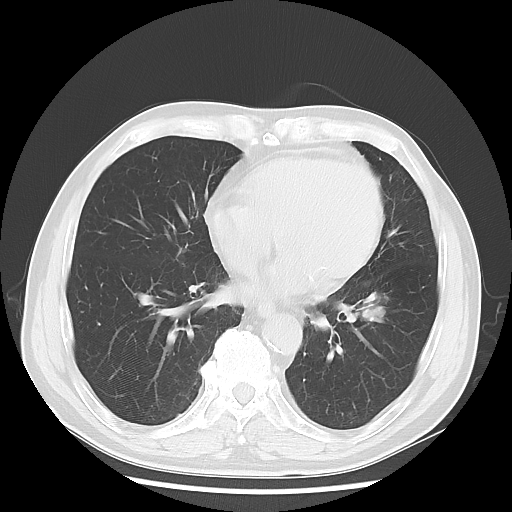
Chest CT, one axial slice; slice 26 of 68 in the series (ordered by position); lung window (W 1500 / L -600 HU); 512 × 512 image matrix, field of view 360 × 360 mm. Male patient, age 71 years. From the clinical record (not read from this slice): clinical TNM (as recorded): T1c N1 M0; histopathological grade: G2-3.
Outlined on this slice (rectangle marked by the reading radiologist):
- lung tumour (recorded histology: adenocarcinoma): bounding box [x1, y1, x2, y2] px = [355, 286, 389, 327]